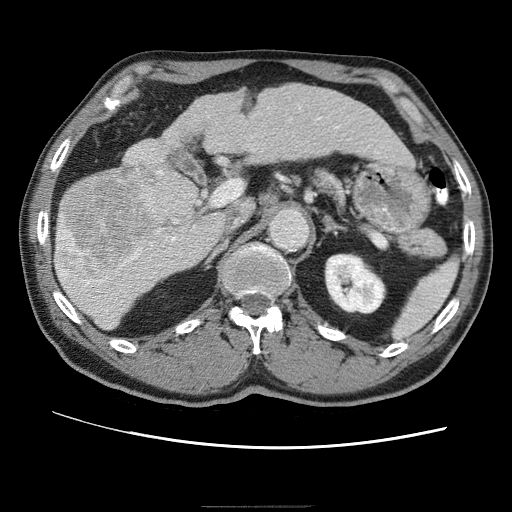
Contrast-enhanced abdominal CT (liver protocol), one axial slice. 120 kVp. One of 2 acquisitions stored at this slice position. Soft-tissue window (W 400 / L 40 HU). 2.5 mm slice thickness. 512 × 512 image matrix, field of view 360 × 360 mm. Case-level facts recorded for this patient, not image findings: diagnosis: hepatocellular carcinoma (patient treated with transarterial chemoembolisation; whether this scan precedes or follows treatment is not stated here); TNM stage (as recorded): Stage-II; Child-Pugh class: A; tumour nodularity: multinodular; tumour size: 2 cm.
Outlined on this slice (semi-automatically segmented with operator editing):
- liver parenchyma outside the tumour (the mass and vessels are separate outlines, so this box may not span the whole liver): bounding box [x1, y1, x2, y2] px = [56, 84, 406, 328]
- mass: [56, 185, 148, 277]
- liver vessels: [60, 155, 192, 278]